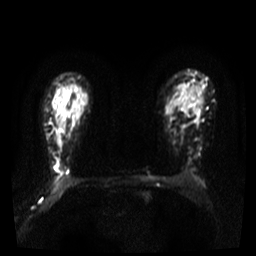
Breast MRI, one axial slice. Slice 27 of 36 in the series (ordered by position). Diffusion-weighted series; image 2 of 4 stored at this slice position (different b-values; order by instance number). 3 T. 5 mm slice thickness. 256 × 256 image matrix. Female patient.
Annotated regions visible in this slice (expert manual segmentation):
- tumour on diffusion-weighted imaging: bounding box [x1, y1, x2, y2] px = [60, 164, 65, 171]